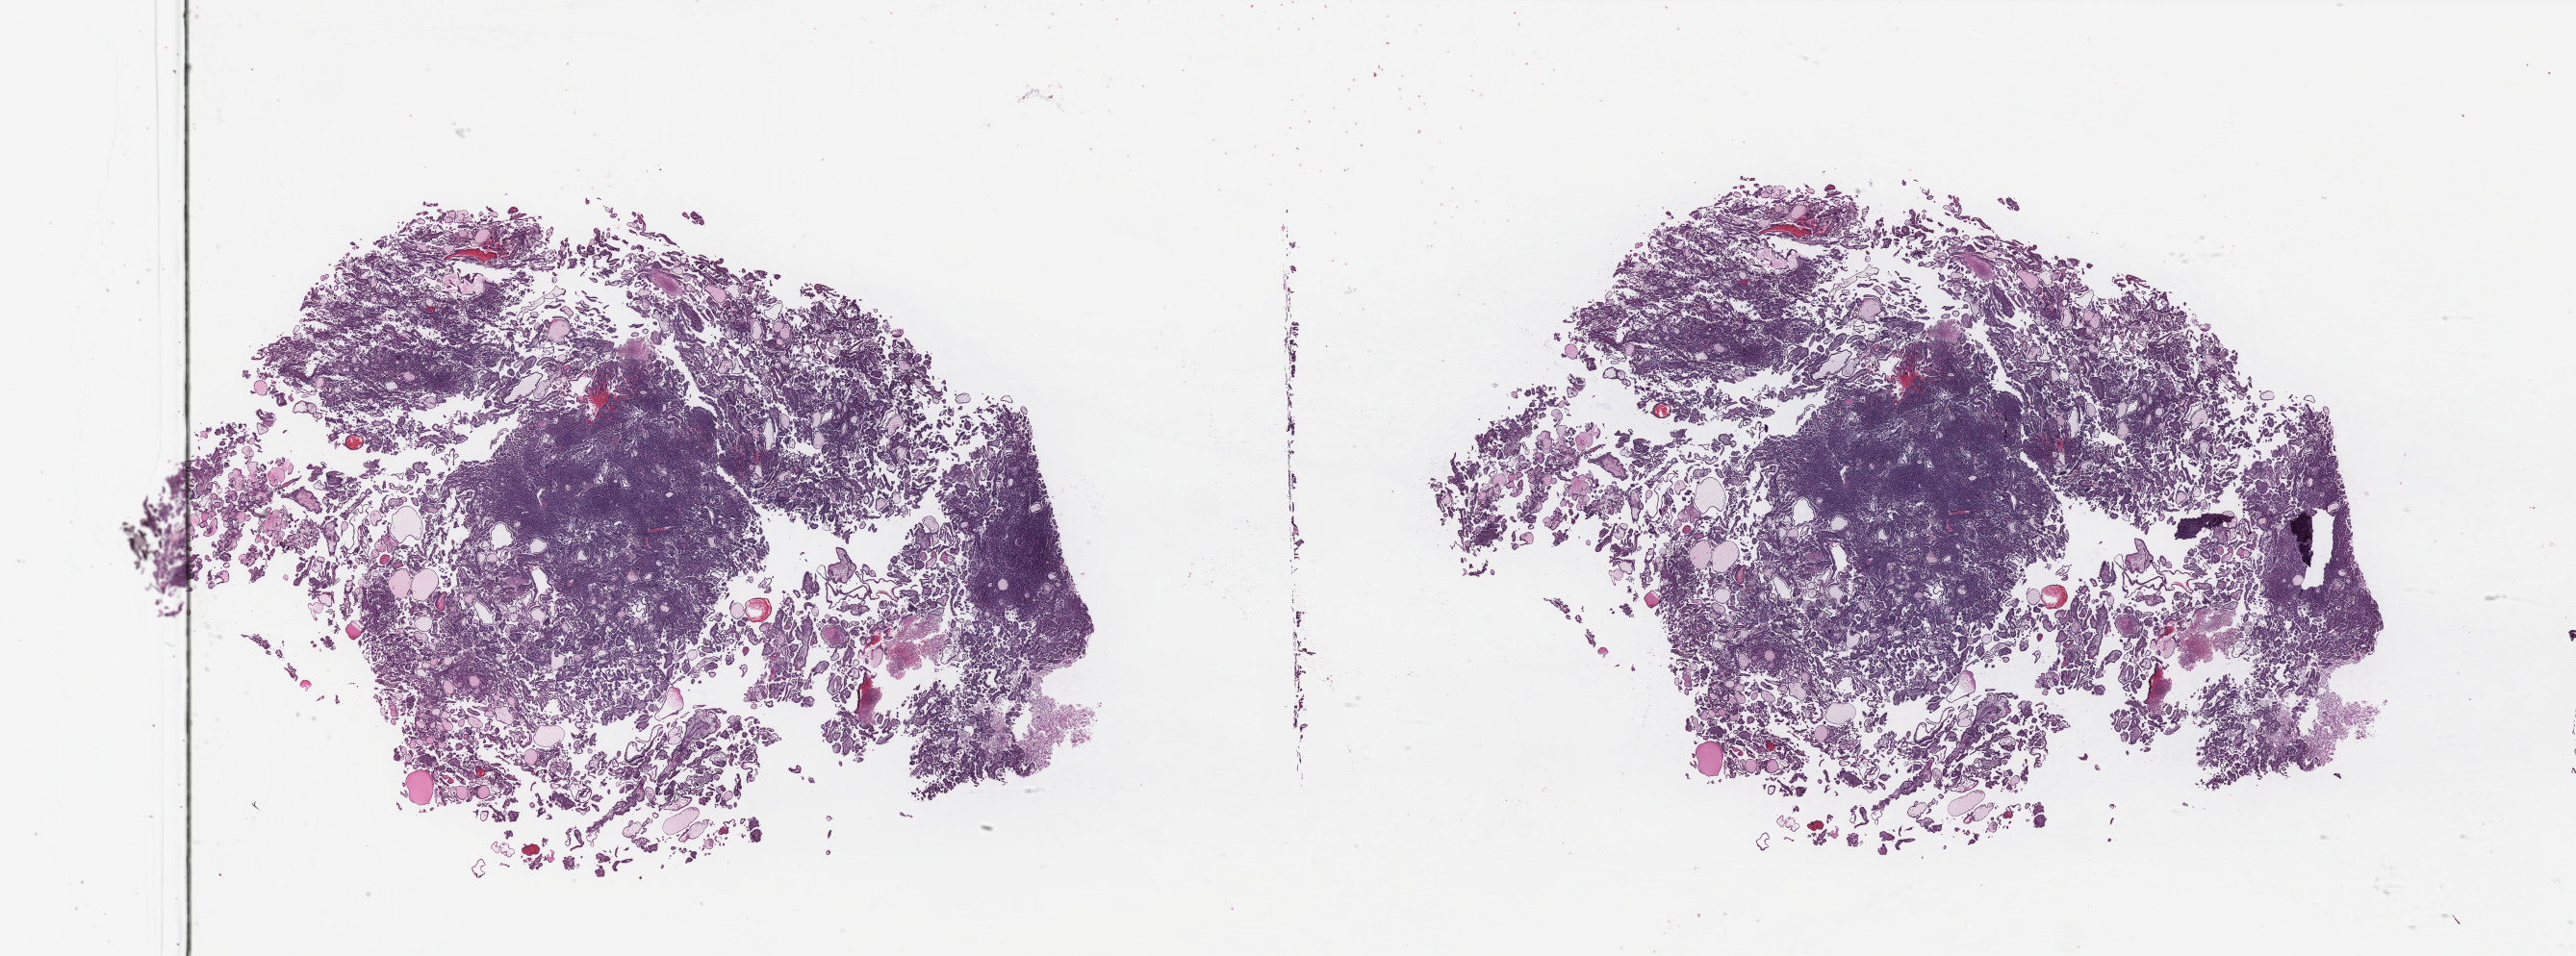
H&E-stained whole-slide image — whole scanned area (about 42.4 x 15.7 mm, from a 40x scan) shown as a low-resolution overview, formalin-fixed paraffin-embedded (FFPE) diagnostic section, sample: primary tumour, kidney. Patient: male, age at initial diagnosis 47 years.
• laterality: right
• pathologic diagnosis: Papillary adenocarcinoma, NOS
• AJCC pathologic stage: I